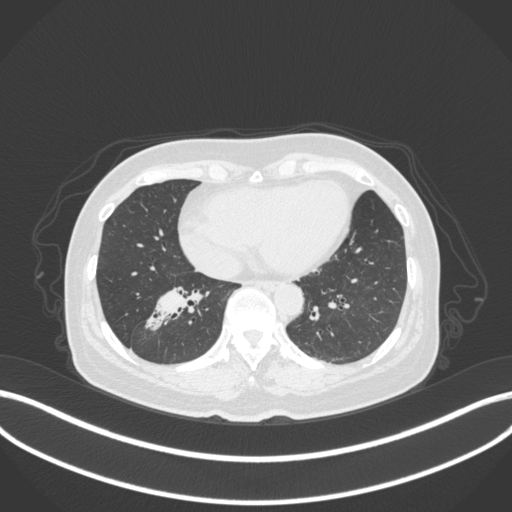
Chest CT, one axial slice; 120 kVp; lung window (W 1500 / L -600 HU); 512 × 512 image matrix. Female patient, age 67 years. Case-level facts recorded for this patient, not image findings: clinical TNM (as recorded): T1c N1 M0; histopathological grade: G2-3.
Outlined on this slice (rectangle marked by the reading radiologist):
- lung tumour (recorded histology: adenocarcinoma): bounding box [x1, y1, x2, y2] px = [141, 284, 213, 334]